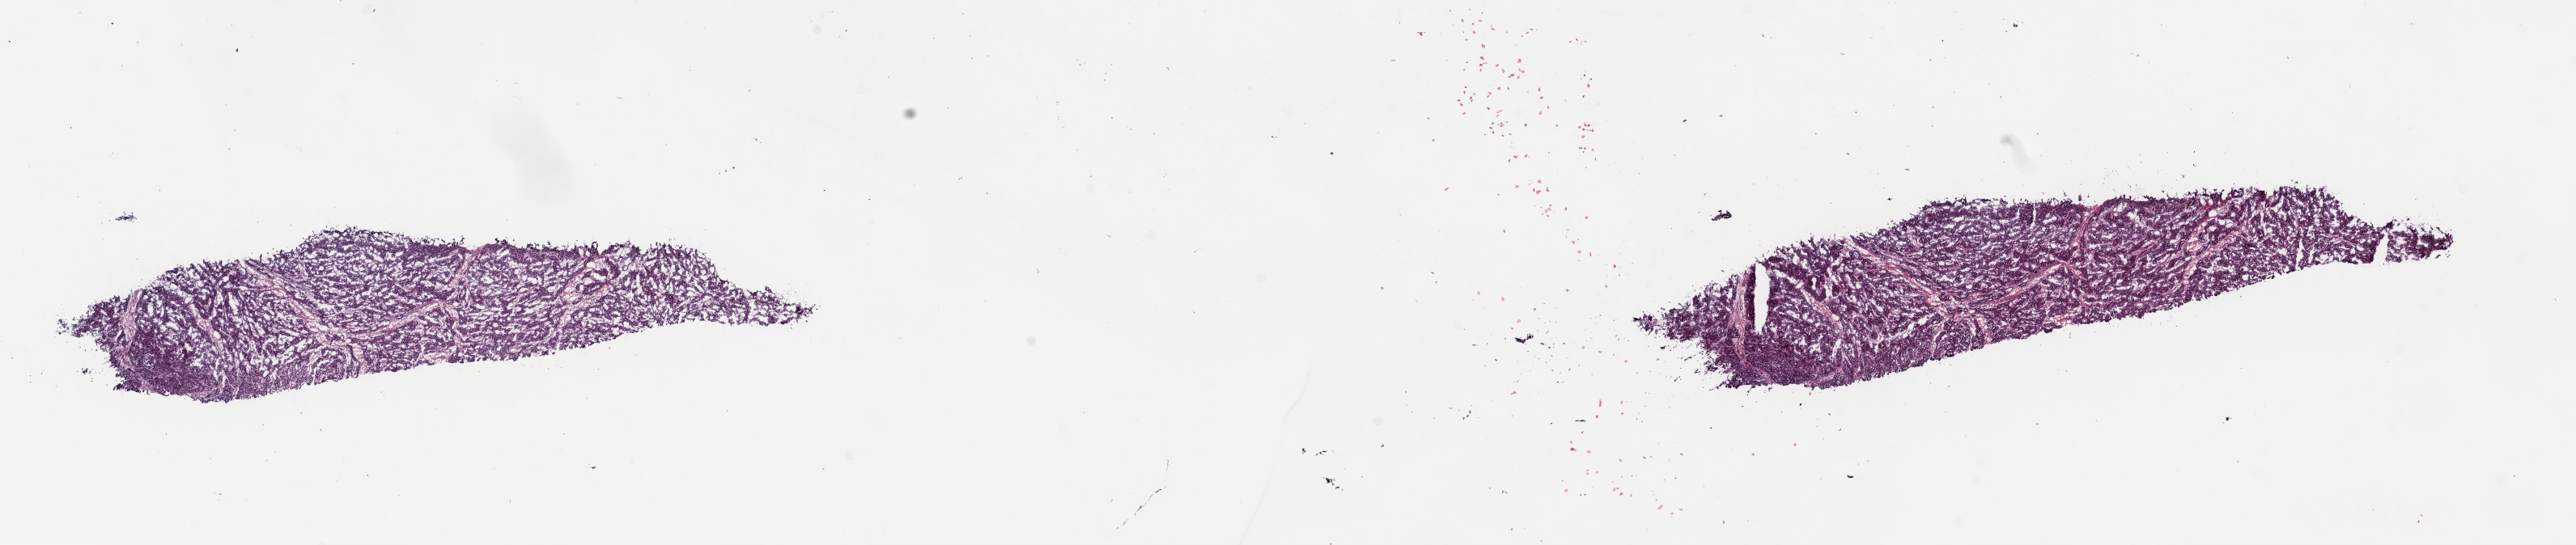
Hematoxylin and eosin (H&E) stained whole-slide image, a low-resolution overview of the entire scanned area, about 25.1 x 5.3 mm (acquisition: 40x scan). Frozen section from the top of the tissue portion. Kidney, primary tumour sample. Female patient; age at initial diagnosis 43 years. Slide review estimates, as recorded: tumour cells 80%, tumour nuclei 95%, normal cells 0%, stromal cells 20%, necrosis 0%. Infiltration values recorded for this section: lymphocyte infiltration 0%, monocyte infiltration 0%, neutrophil infiltration 0%.
- laterality: right
- AJCC pathologic stage: I
- diagnosis: Papillary adenocarcinoma, NOS